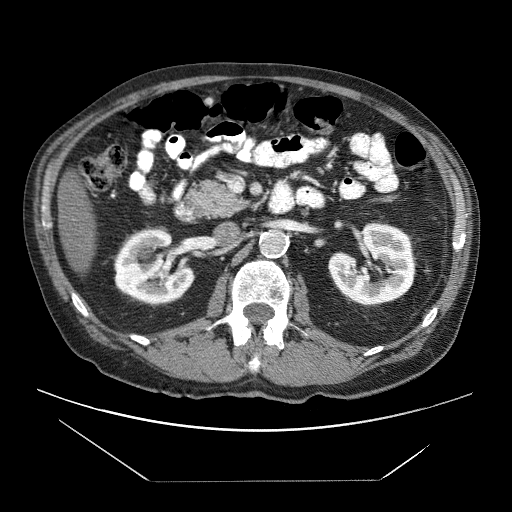
Contrast-enhanced abdominal CT (liver protocol), one axial slice; position 13 of 83 along the scan axis; reconstruction kernel STANDARD; 120 kVp; soft-tissue window (W 400 / L 40 HU); 2.5 mm slice thickness; 512 × 512 image matrix. Case-level facts recorded for this patient, not image findings: diagnosis: hepatocellular carcinoma (patient treated with transarterial chemoembolisation; whether this scan precedes or follows treatment is not stated here); TNM stage (as recorded): Stage-IVB; Child-Pugh class: B.
Structures marked on this image (semi-automatic segmentation, software-assisted and operator-edited):
- liver parenchyma outside the tumour (the mass and vessels are separate outlines, so this box may not span the whole liver): box from (x=58, y=176) to (x=97, y=274) px